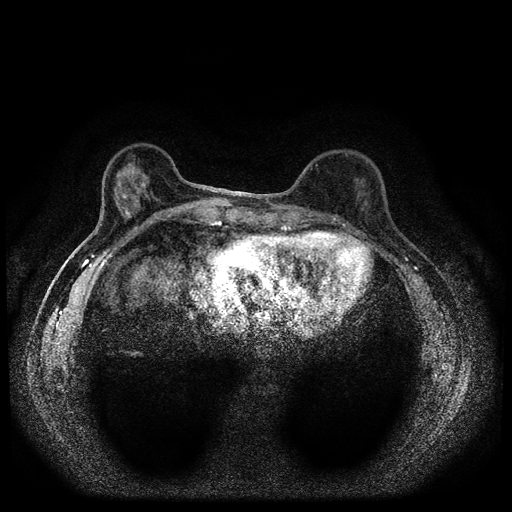
Breast MRI (dynamic contrast-enhanced, multi-phase), one axial slice; slice 32 of 112 in the series (ordered by position); dynamic contrast-enhanced series, time point 2 of 5 at this slice position (early post-contrast); 1.5 T; TE 2.7 ms, TR 5.4 ms; 512 × 512 image matrix, field of view 320 × 320 mm. Female patient, age 61 years.
Annotated regions visible in this slice (semi-automatically segmented with operator editing):
- breast lesion (labelled benign in the annotation): bounding box [x1, y1, x2, y2] px = [115, 162, 147, 220]